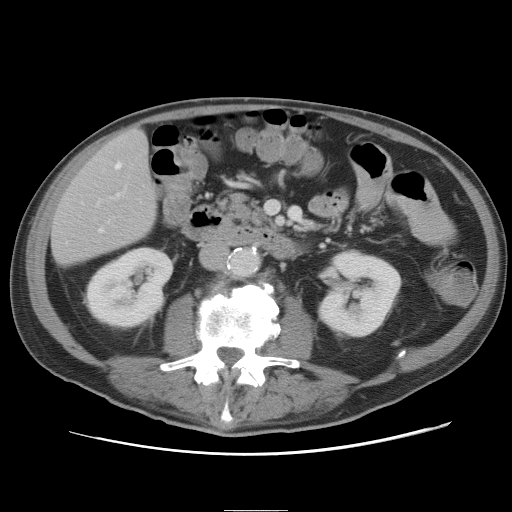
Contrast-enhanced abdominal CT, one axial slice. Position 17 of 89 along the scan axis. Intravenous contrast given. Soft-tissue window (W 400 / L 40 HU). 5 mm slice thickness. 512 × 512 image matrix, field of view 375 × 375 mm. Male patient, age 69 years. Case-level facts recorded for this patient, not image findings: diagnosis: colorectal cancer liver metastases, imaged before liver resection.
Annotated regions visible in this slice (expert manual segmentation):
- hepatic veins: bounding box <100,162,122,232> (left, top, right, bottom; pixels)
- liver: <52,129,157,267>
- planned liver remnant (the part of the liver to remain after resection): <53,128,157,266>
- portal vein (with intrahepatic branches): <117,191,124,196>